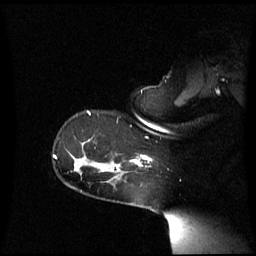
Breast MRI (dynamic contrast-enhanced), one sagittal slice. Slice 48 of 60 in the series (ordered by position). Dynamic contrast-enhanced series, image 2 of 3 at this slice position (ordered by acquisition). 1.5 T. TE 4.2 ms, TR 8.4 ms. 256 × 256 image matrix, field of view 270 × 270 mm. Patient: female, 39 years. From the clinical record (not read from this slice): setting: breast cancer imaged before/during neoadjuvant chemotherapy; receptor status: triple-negative.
Annotated regions visible in this slice (semi-automatic segmentation, software-assisted and operator-edited):
- analysis volume of interest (the breast-tissue region the enhancement analysis was run in; not a lesion): bounding box [x1, y1, x2, y2] px = [117, 156, 151, 176]
- tumour enhancement mask (voxels above the 70 % enhancement threshold inside the analysis volume of interest): [131, 156, 151, 164]